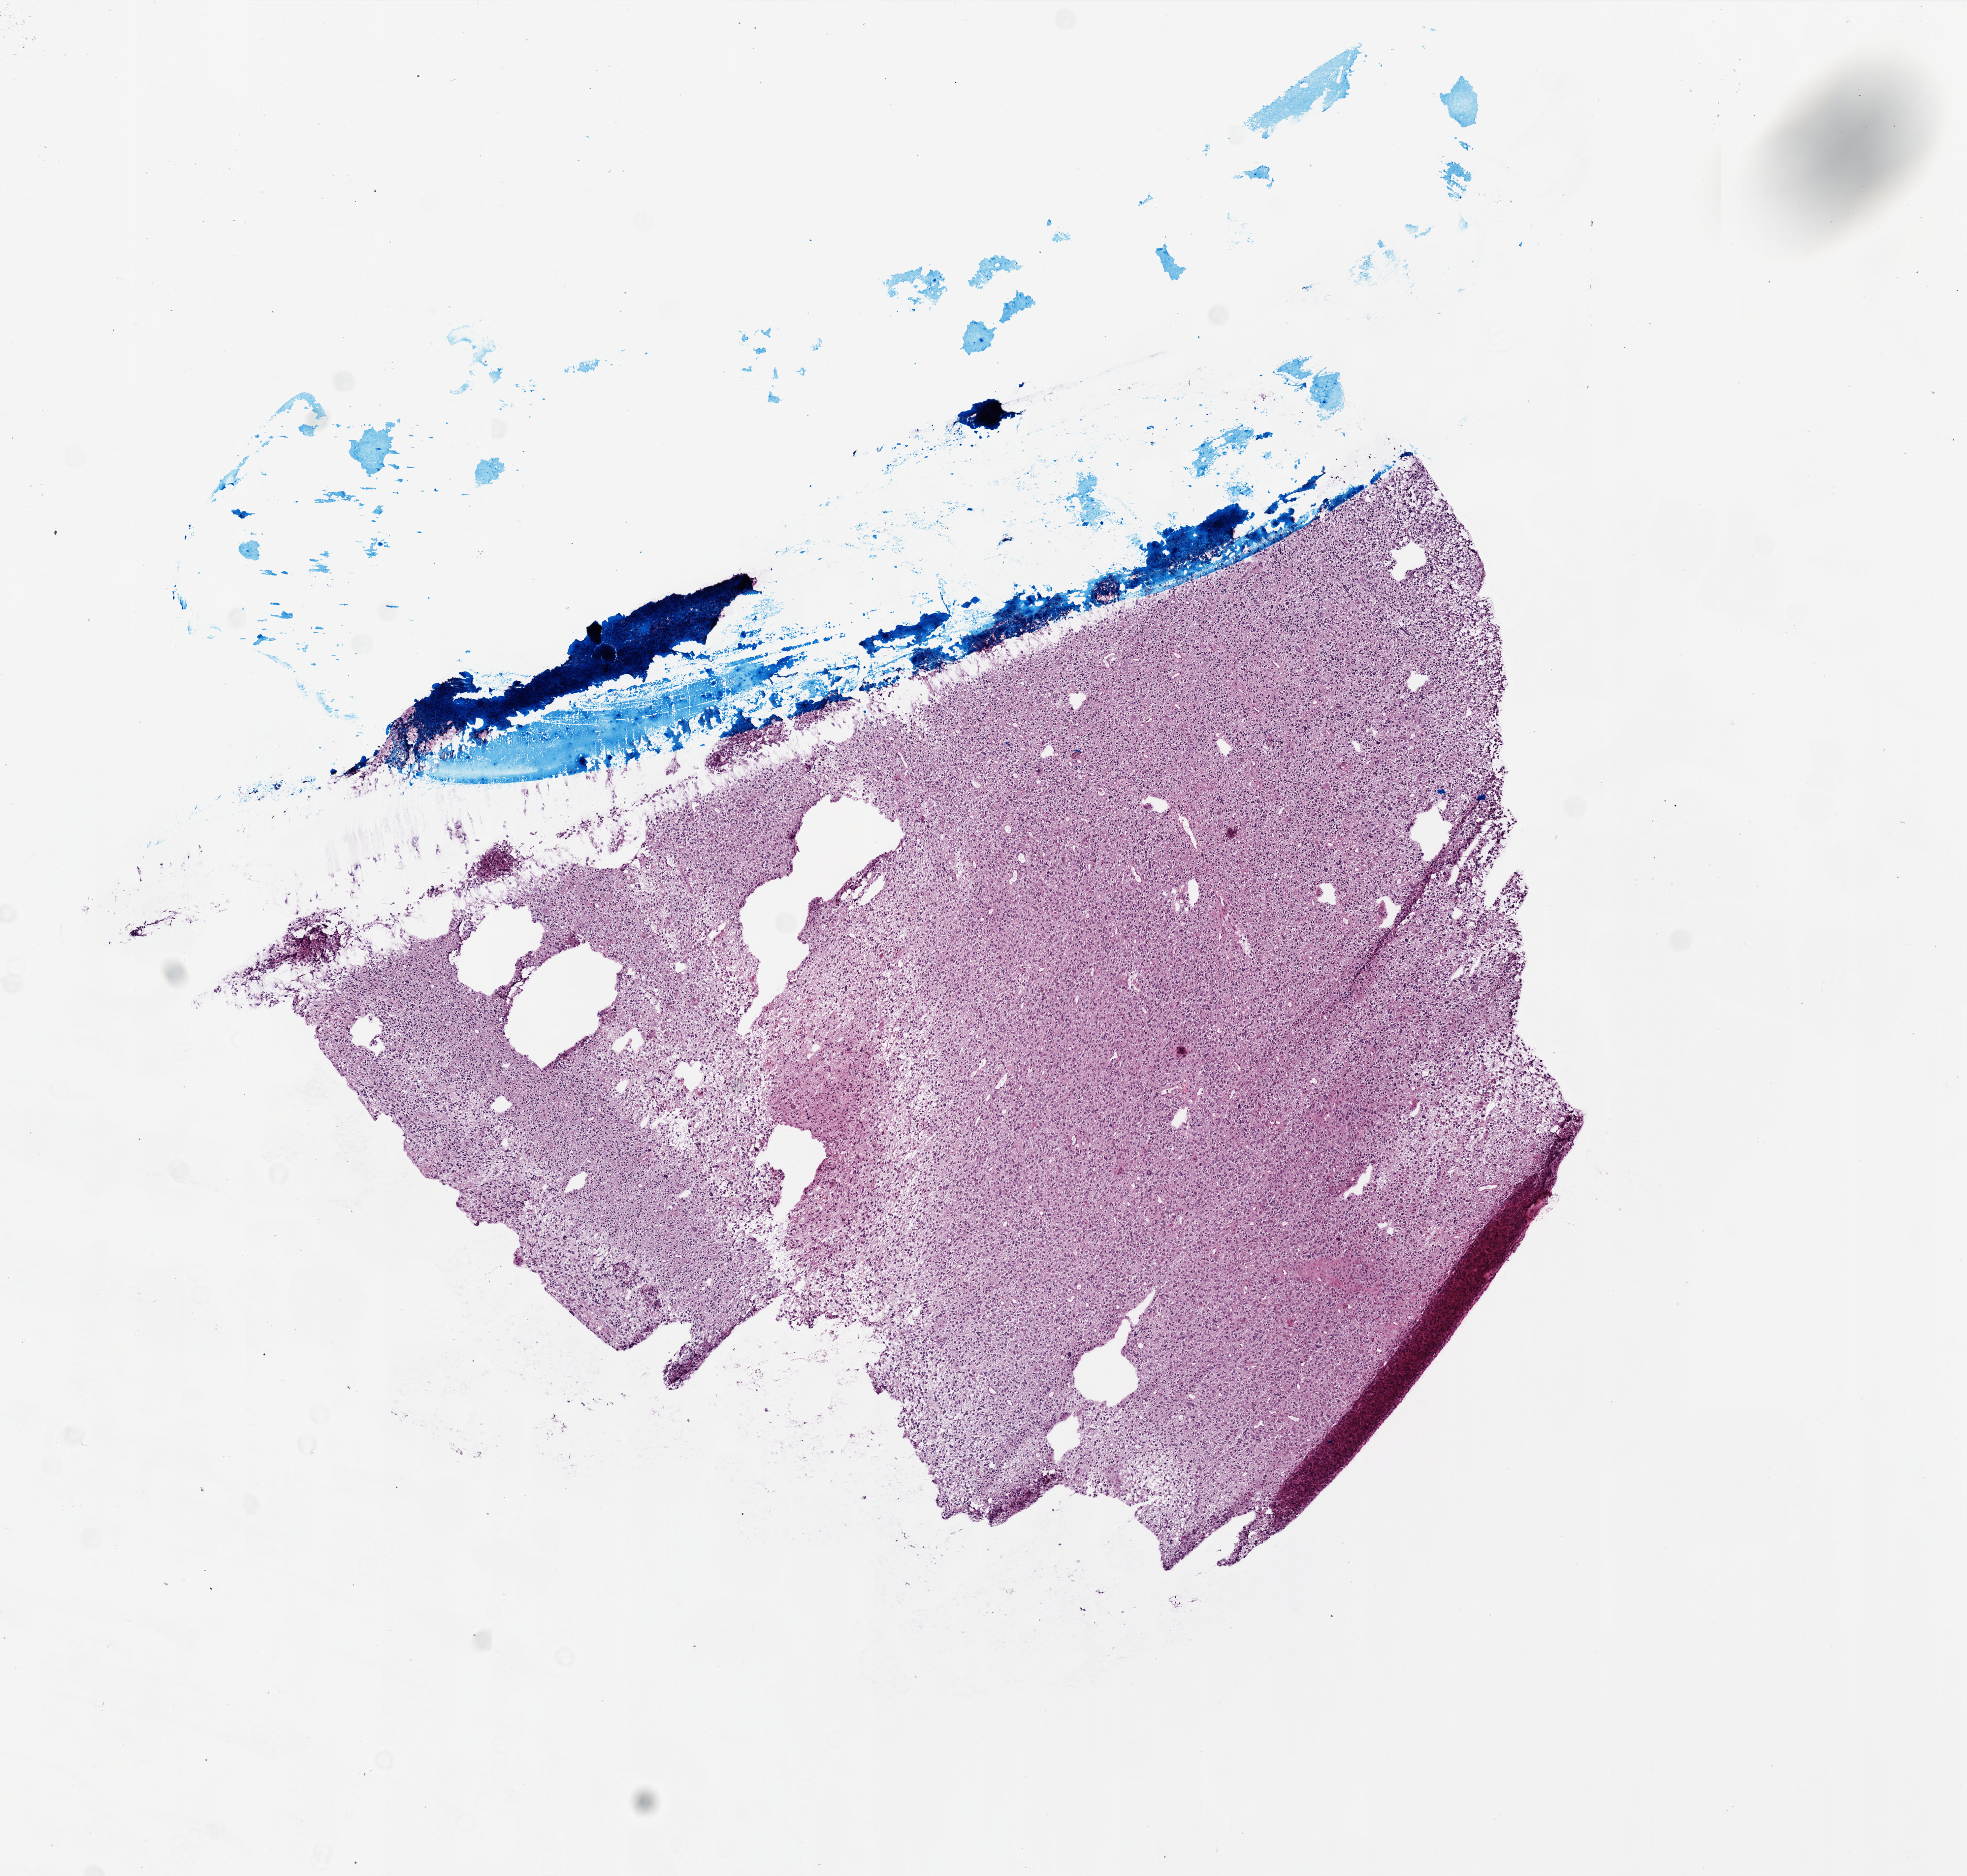
Digitized Hematoxylin and eosin (H&E) stained tissue section (whole slide) — whole scanned area (about 8.0 x 7.6 mm, from a 20x scan) shown as a low-resolution overview, frozen section, sample: primary tumour, brain. Male patient; age at initial diagnosis 14 years. Composition of this section per pathologist review: tumour cells 100%, tumour nuclei 100%, normal cells 0%, stromal cells 0%, necrosis 0%.
Pathologic diagnosis: Glioblastoma.